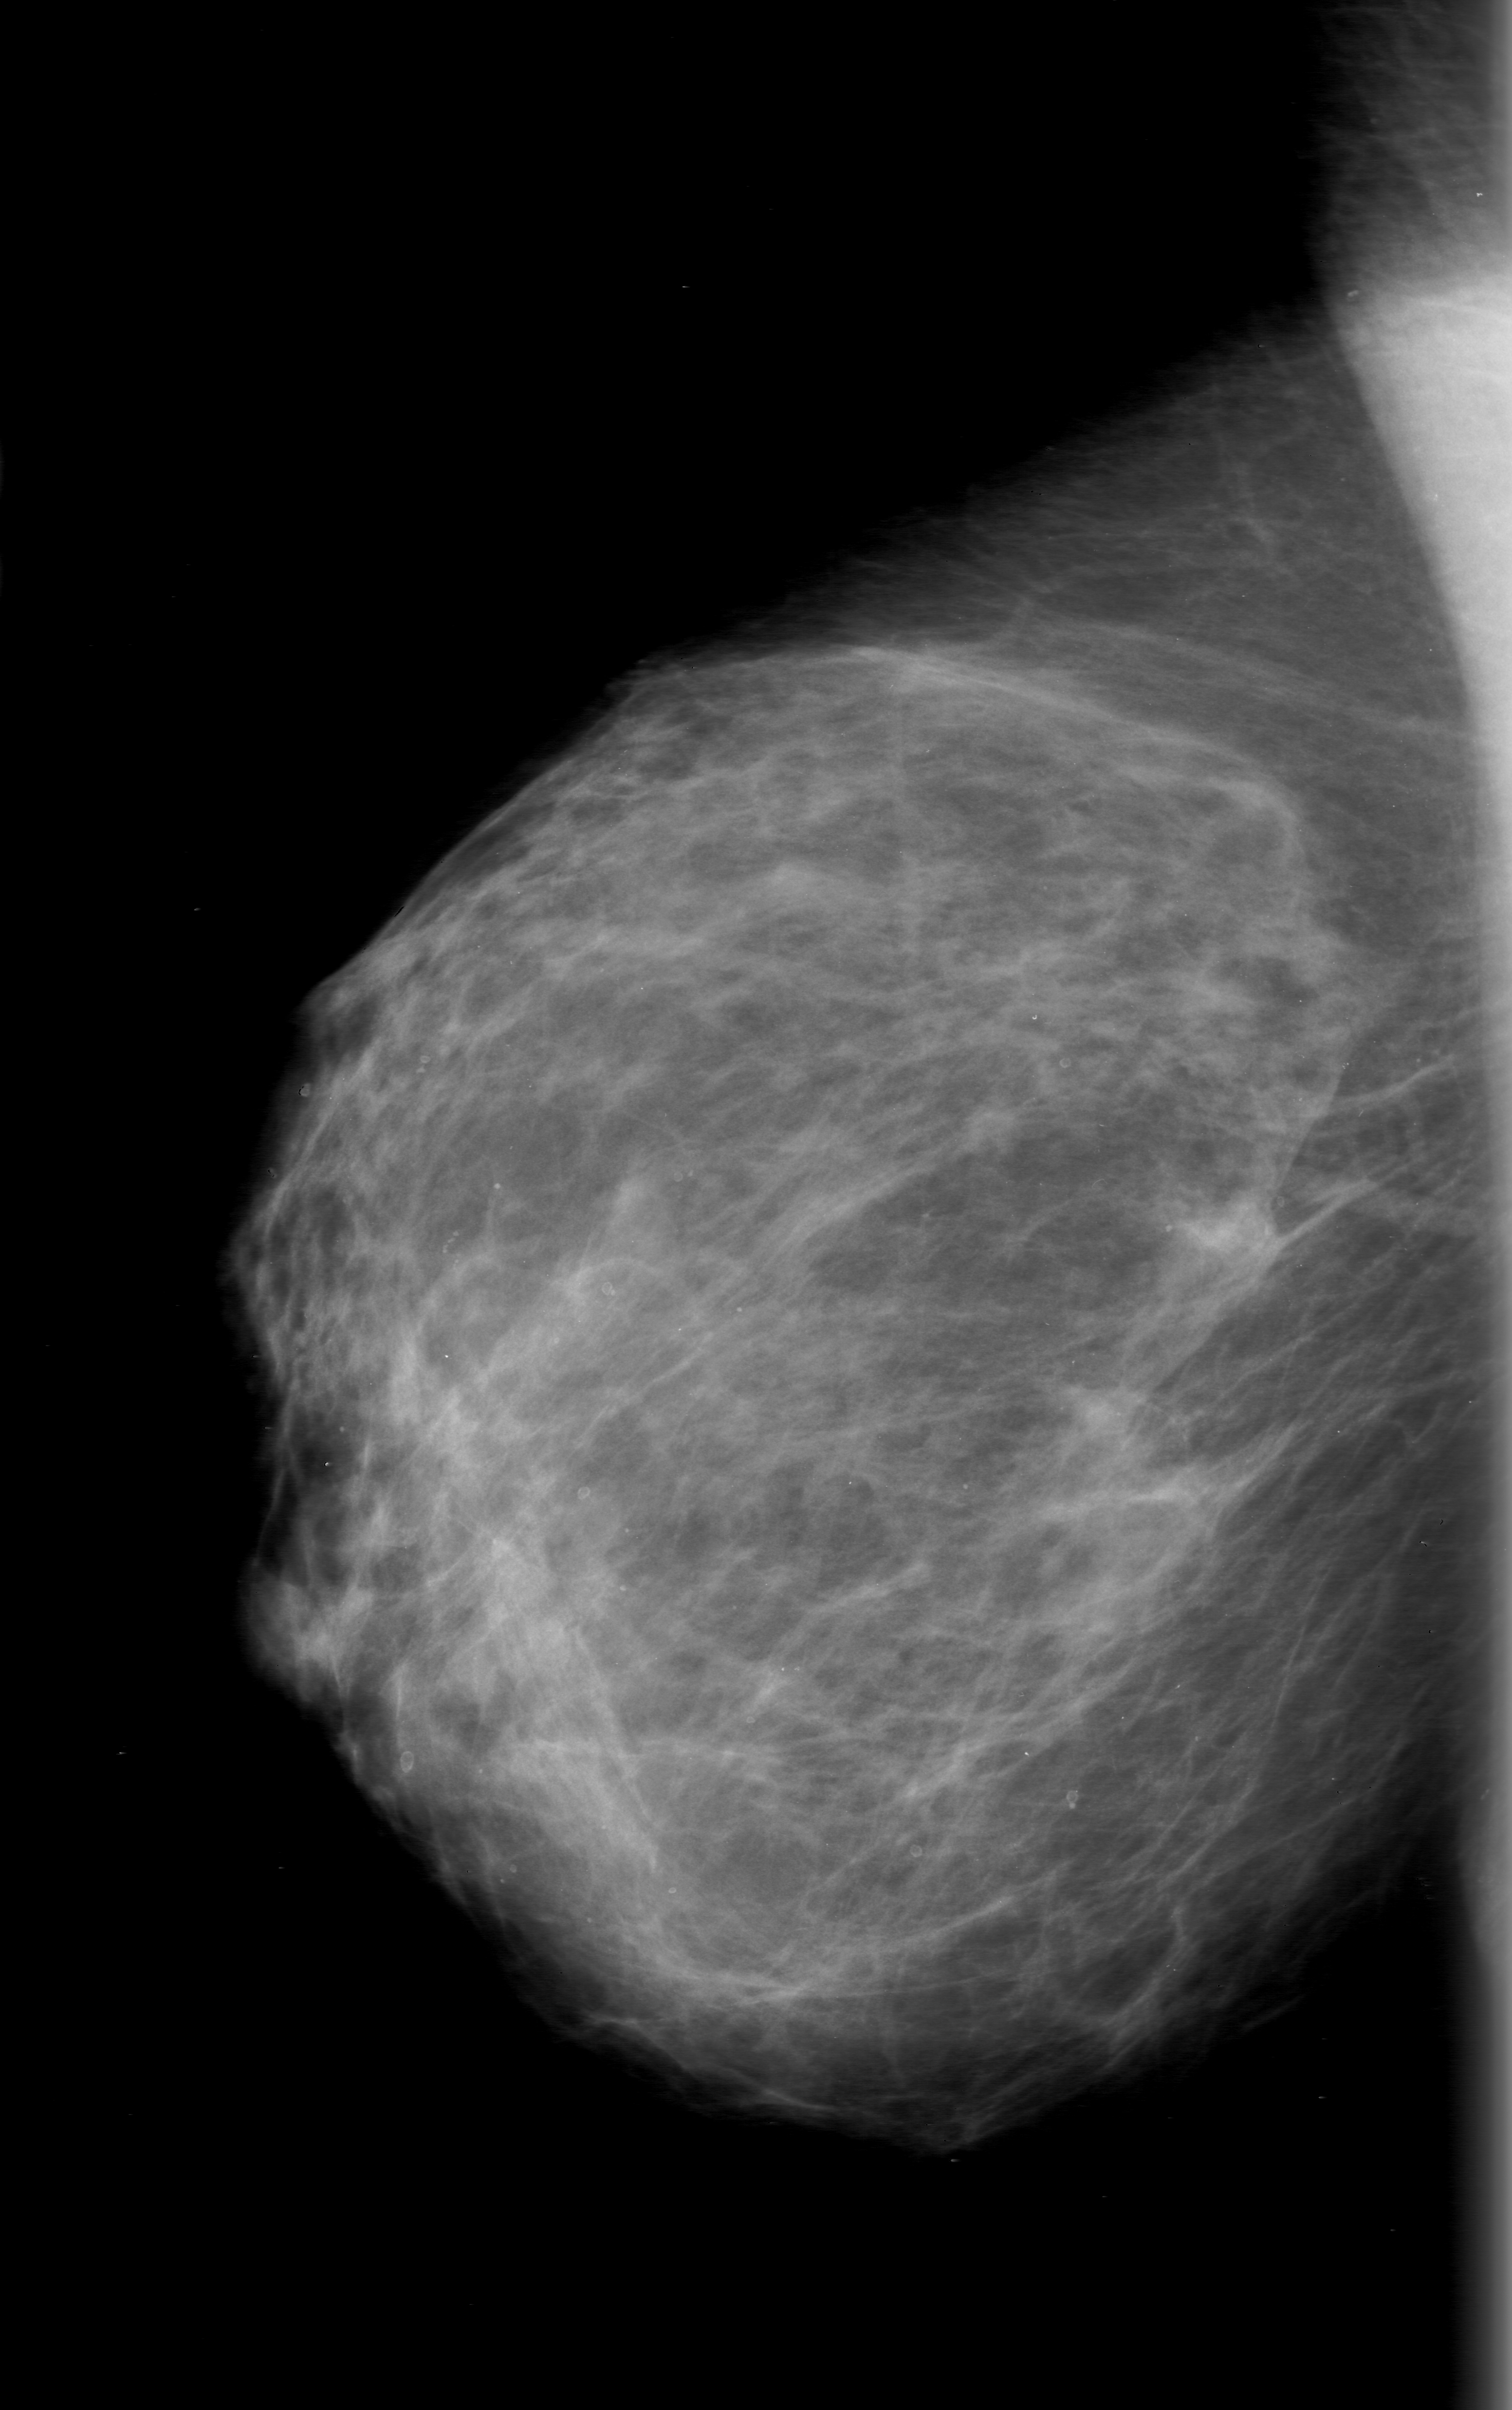
Mammogram (digitized film). Right breast. Mediolateral oblique (MLO) view. BI-RADS breast density category 2 (scale 1–4). 1512 × 2410 image matrix.
Expert-marked regions of interest on this image (one box per marked abnormality):
- mass, shape architectural distortion; BI-RADS assessment category 0; subtlety rating 4 on a 1 (subtle) to 5 (obvious) scale; pathology (as recorded): malignant: box from (x=1002, y=1418) to (x=1238, y=1636) px